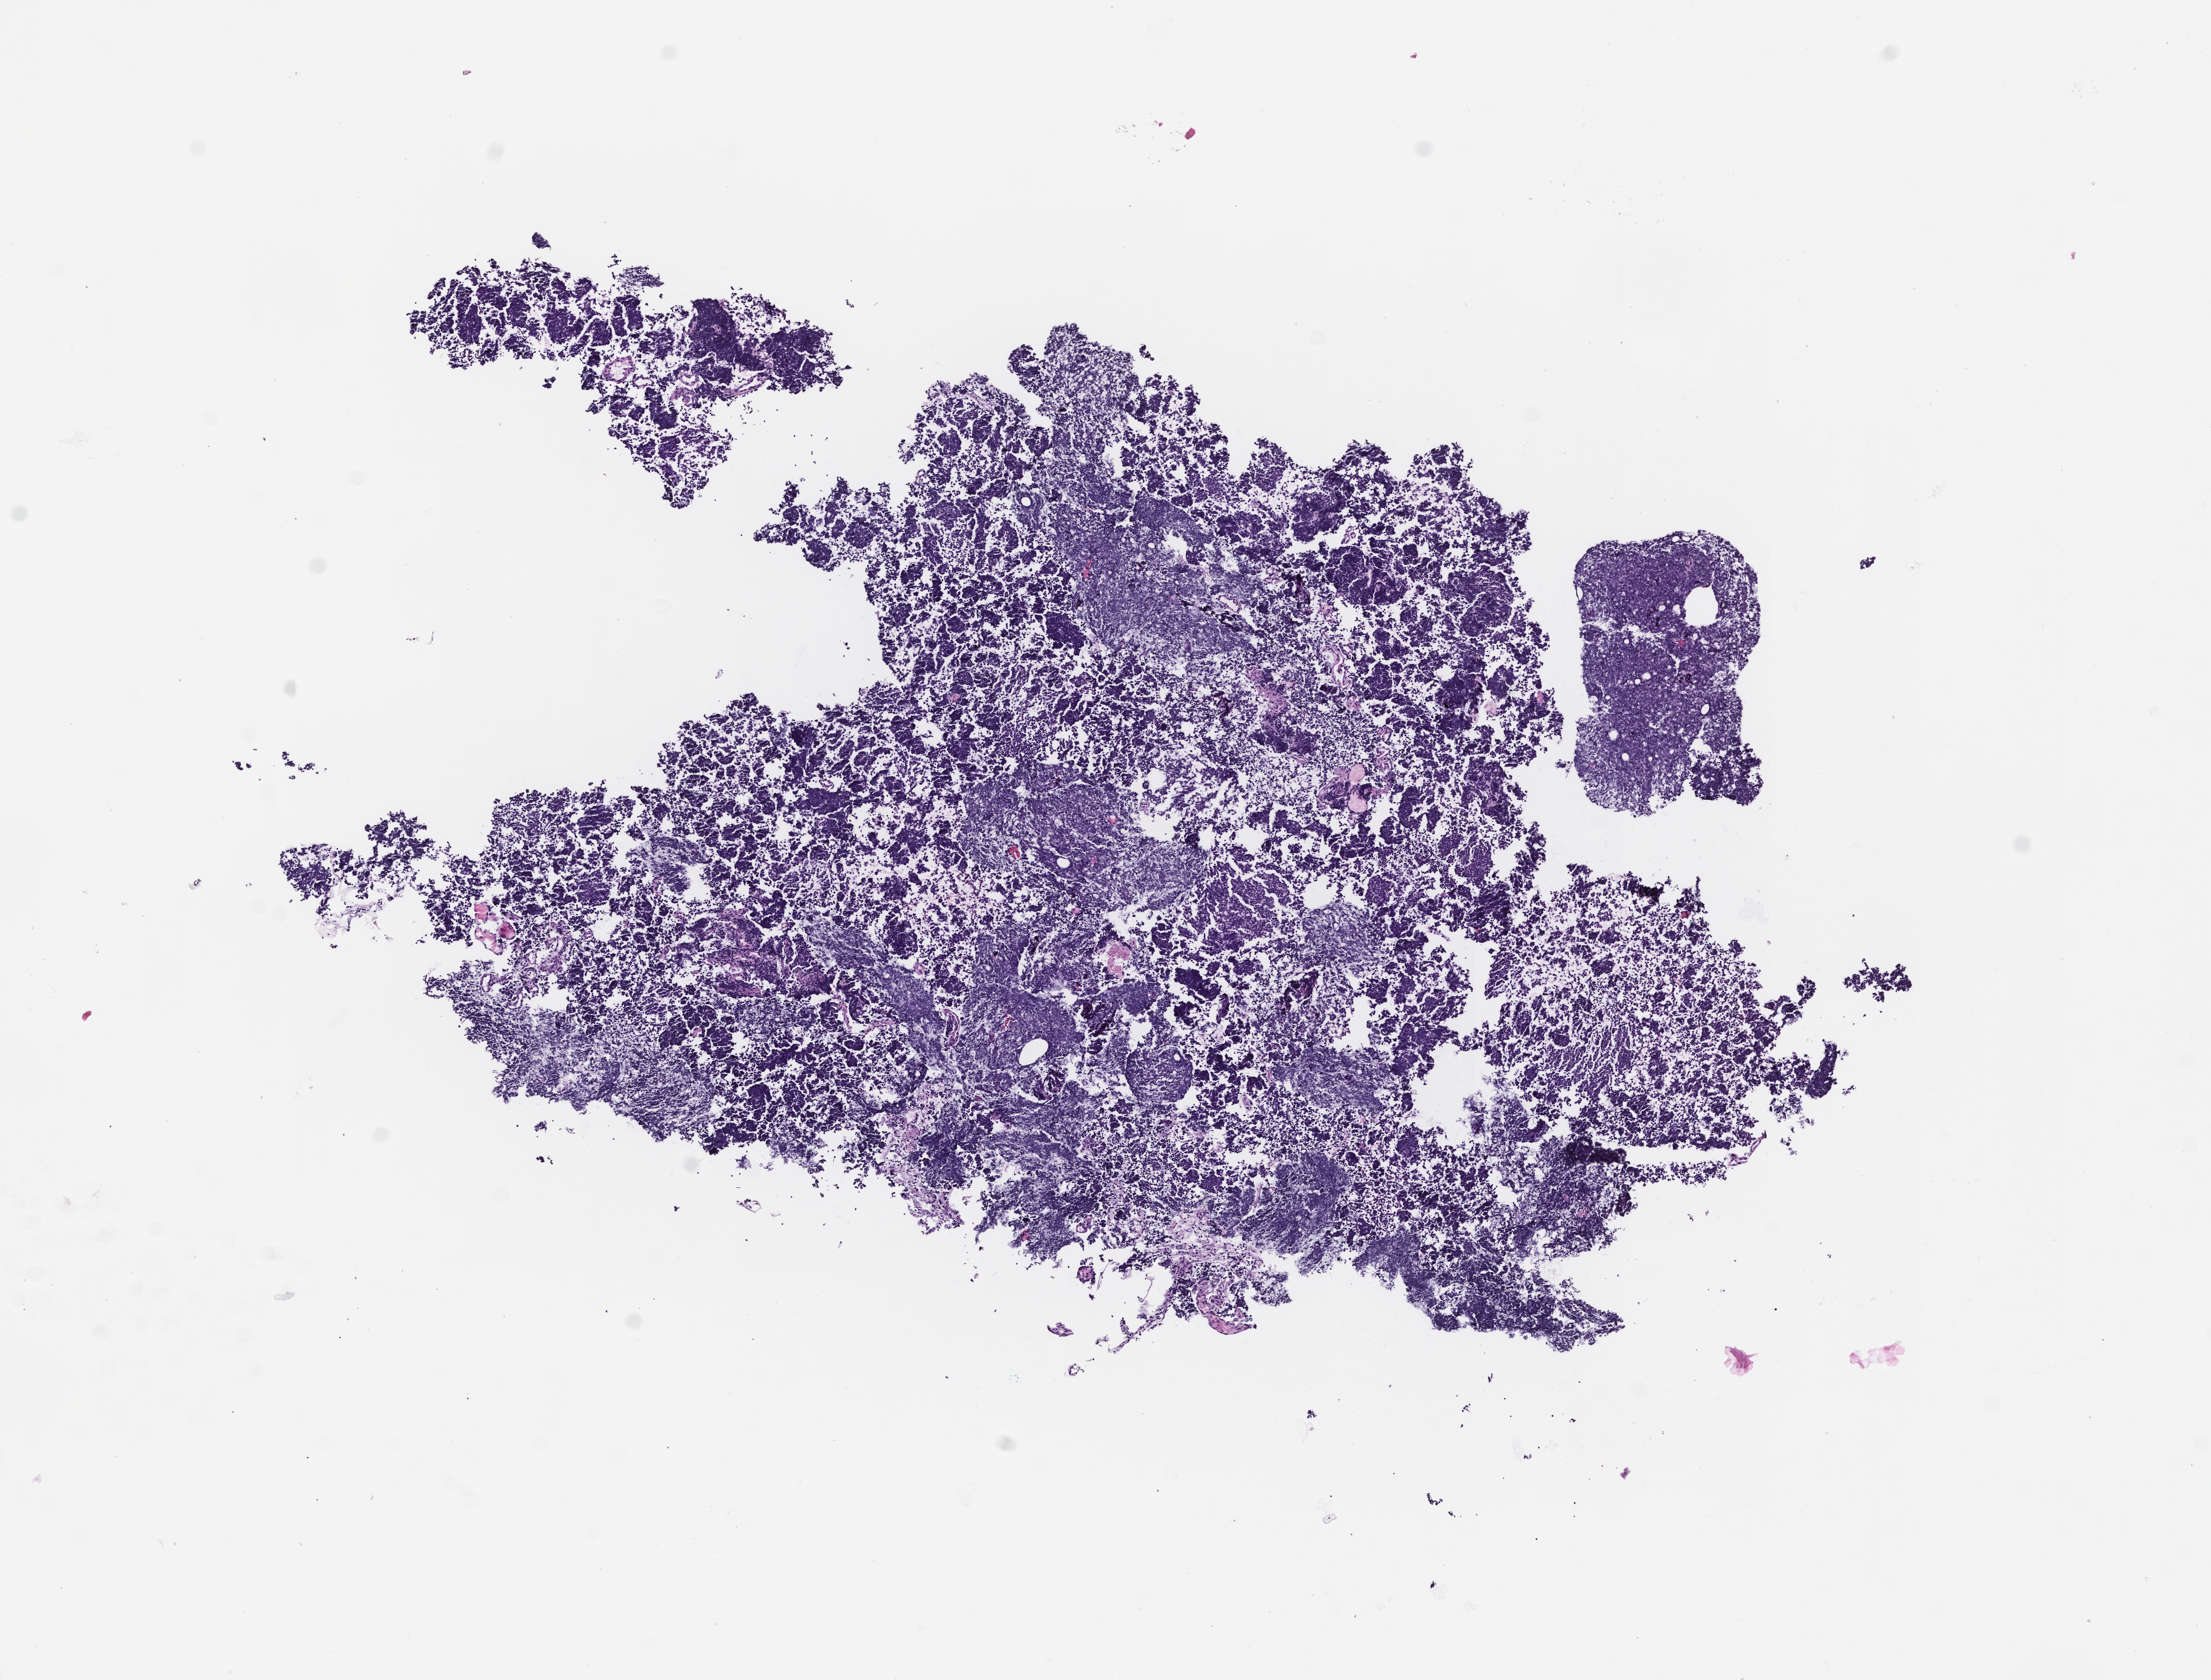
Whole-slide image, hematoxylin and eosin (H&E) stain — shown as a low-resolution overview of the whole scanned area (about 7.5 x 5.7 mm). Formalin-fixed, paraffin-embedded (FFPE) tissue. Site: lung. Specimen time point: archival tissue. Patient sex: male.
* this section: primary tumour tissue
* diagnosis: Non-Small Cell Lung Carcinoma